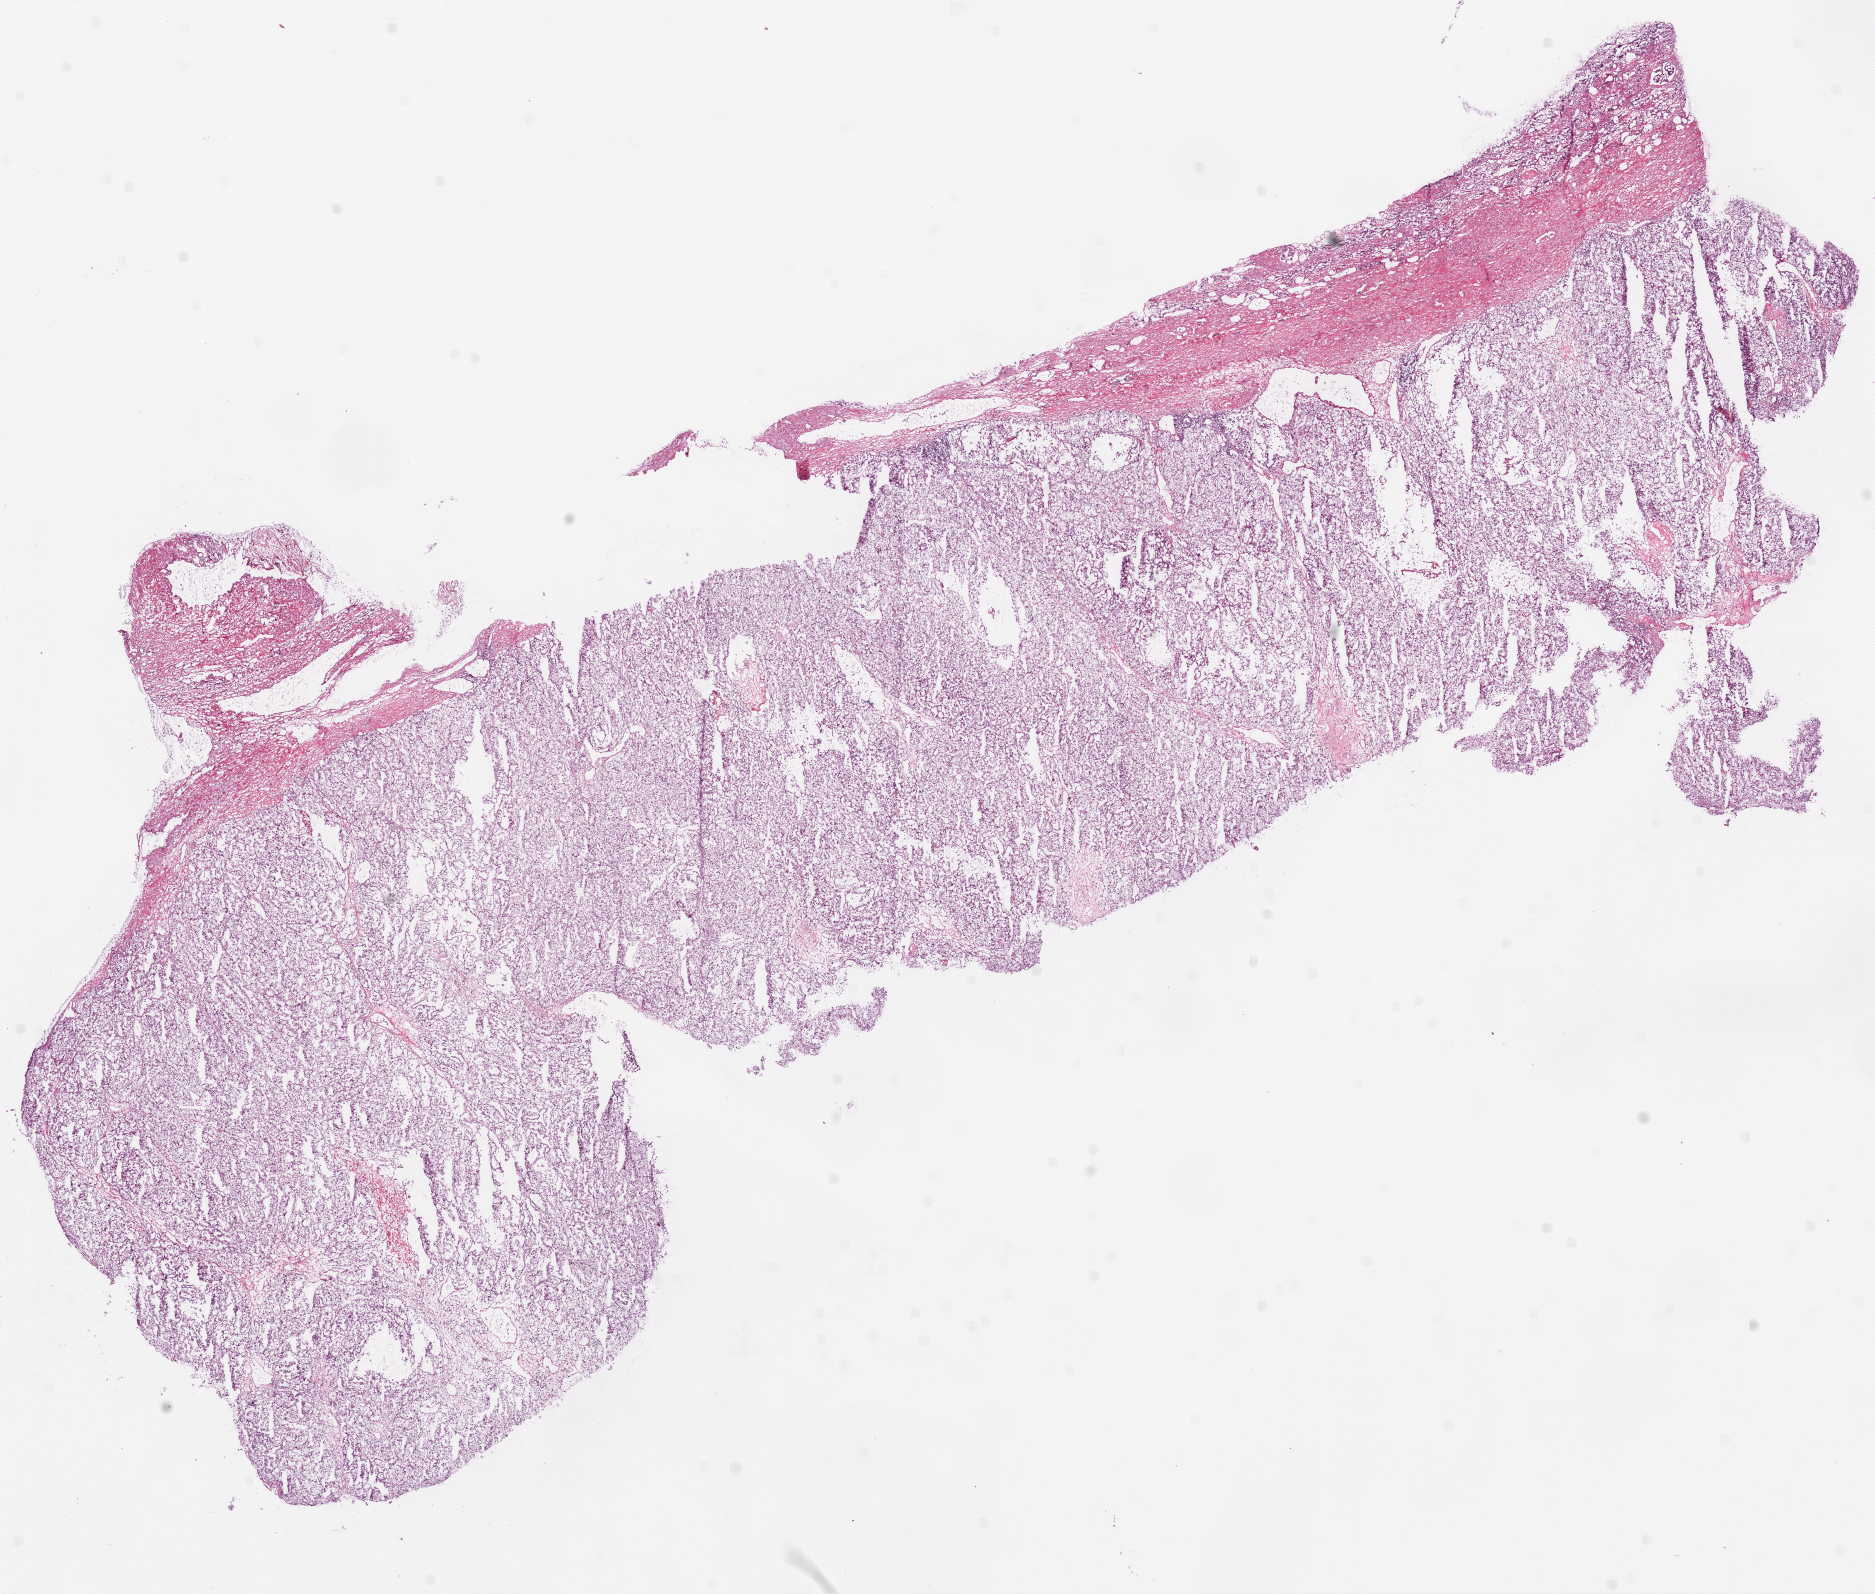
Digitized Hematoxylin and eosin (H&E) stained tissue section (whole slide) — a low-resolution overview of the entire scanned area, about 15.0 x 12.8 mm; frozen section; kidney, primary tumour sample. Female patient; age at initial diagnosis 60 years. Histologic grade: G3 (poorly differentiated). Composition of this section per pathologist review: tumour cells 85%, tumour nuclei 88%, normal cells 5%, stromal cells 10%, necrosis 0%.
- AJCC pathologic stage: III
- diagnosis: Clear cell adenocarcinoma, NOS
- lymph nodes positive (case pathology): 0 of 9 examined
- laterality: right